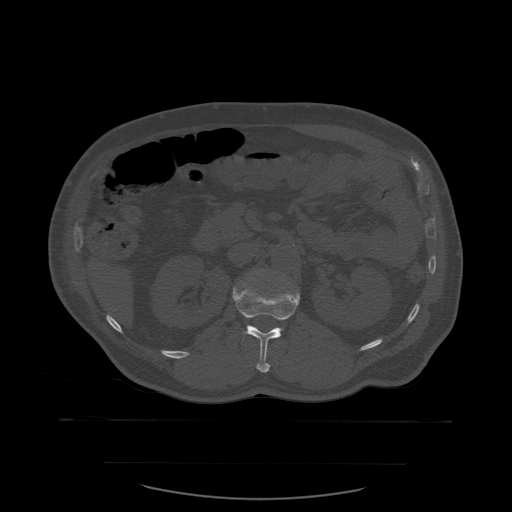
CT including the spine, one axial slice. Position 242 of 590 along the scan axis. Bone window (W 1800 / L 400 HU). 512 × 512 image matrix, field of view 479 × 479 mm. Patient age 71 years. From the clinical record (not read from this slice): primary cancer: lung; vertebrae with lytic lesions (as recorded): T1, T2, L5, S1.
Structures marked on this image (semi-automatically segmented with operator editing):
- L1 vertebra: bounding box [x1, y1, x2, y2] px = [232, 286, 300, 373]
- L2 vertebra: [236, 272, 285, 288]